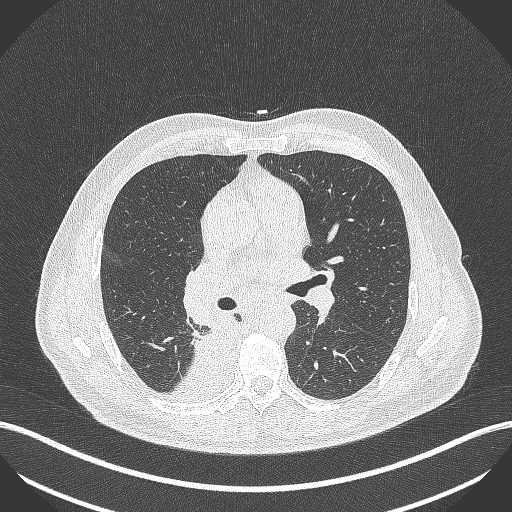
Chest CT, one axial slice; reconstruction kernel B70f; 100 kVp; lung window (W 1500 / L -600 HU); 1 mm slice thickness; 512 × 512 image matrix, field of view 400 × 400 mm. Patient: male, 61 years. Case-level facts recorded for this patient, not image findings: clinical TNM (as recorded): T1 N0 M0.
Annotated regions visible in this slice (rectangle marked by the reading radiologist):
- lung tumour (recorded histology: small cell carcinoma): bounding box (x1, y1, x2, y2) in pixels: (193, 313, 243, 375)